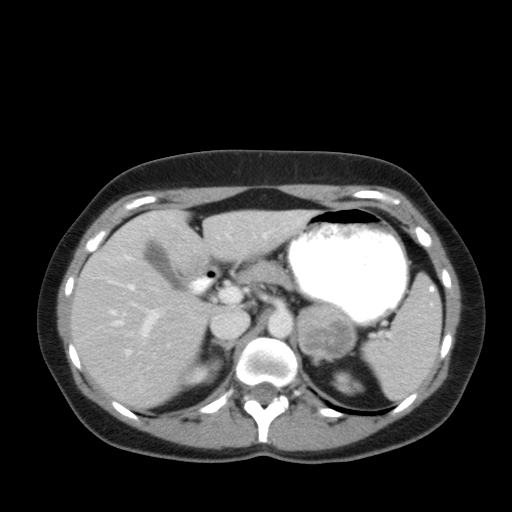
Contrast-enhanced abdominal CT, one axial slice. Position 35 of 92 along the scan axis. Reconstruction kernel FC12. Intravenous contrast given. Soft-tissue window (W 400 / L 40 HU). 5 mm slice thickness. 512 × 512 image matrix, field of view 369 × 369 mm. Female patient, age 35 years. Case-level facts recorded for this patient, not image findings: diagnosis: adrenocortical carcinoma; tumour side: left adrenal; tumour size at pathology: 6.6 cm; Ki-67 index: 5 %; stage (as recorded): 2.
Structures marked on this image (semi-automatically segmented with operator editing):
- mass: box from (x=299, y=306) to (x=352, y=355) px